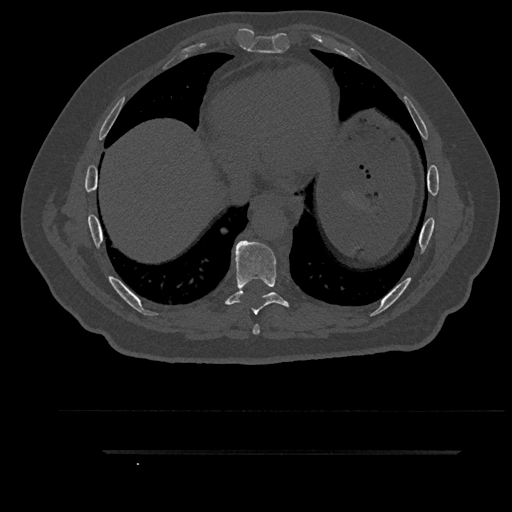
CT including the spine, one axial slice. Slice 476 of 797 in the series (ordered by position). Bone window (W 1800 / L 400 HU). 0.5 mm slice thickness. 512 × 512 image matrix, field of view 432 × 432 mm. Male patient, age 63 years. Case-level facts recorded for this patient, not image findings: primary cancer: renal; vertebrae with lytic lesions (as recorded): T8.
Structures marked on this image (semi-automatic segmentation, software-assisted and operator-edited):
- T7 vertebra: bounding box [x1, y1, x2, y2] px = [253, 325, 260, 335]
- T8 vertebra: [220, 240, 294, 315]